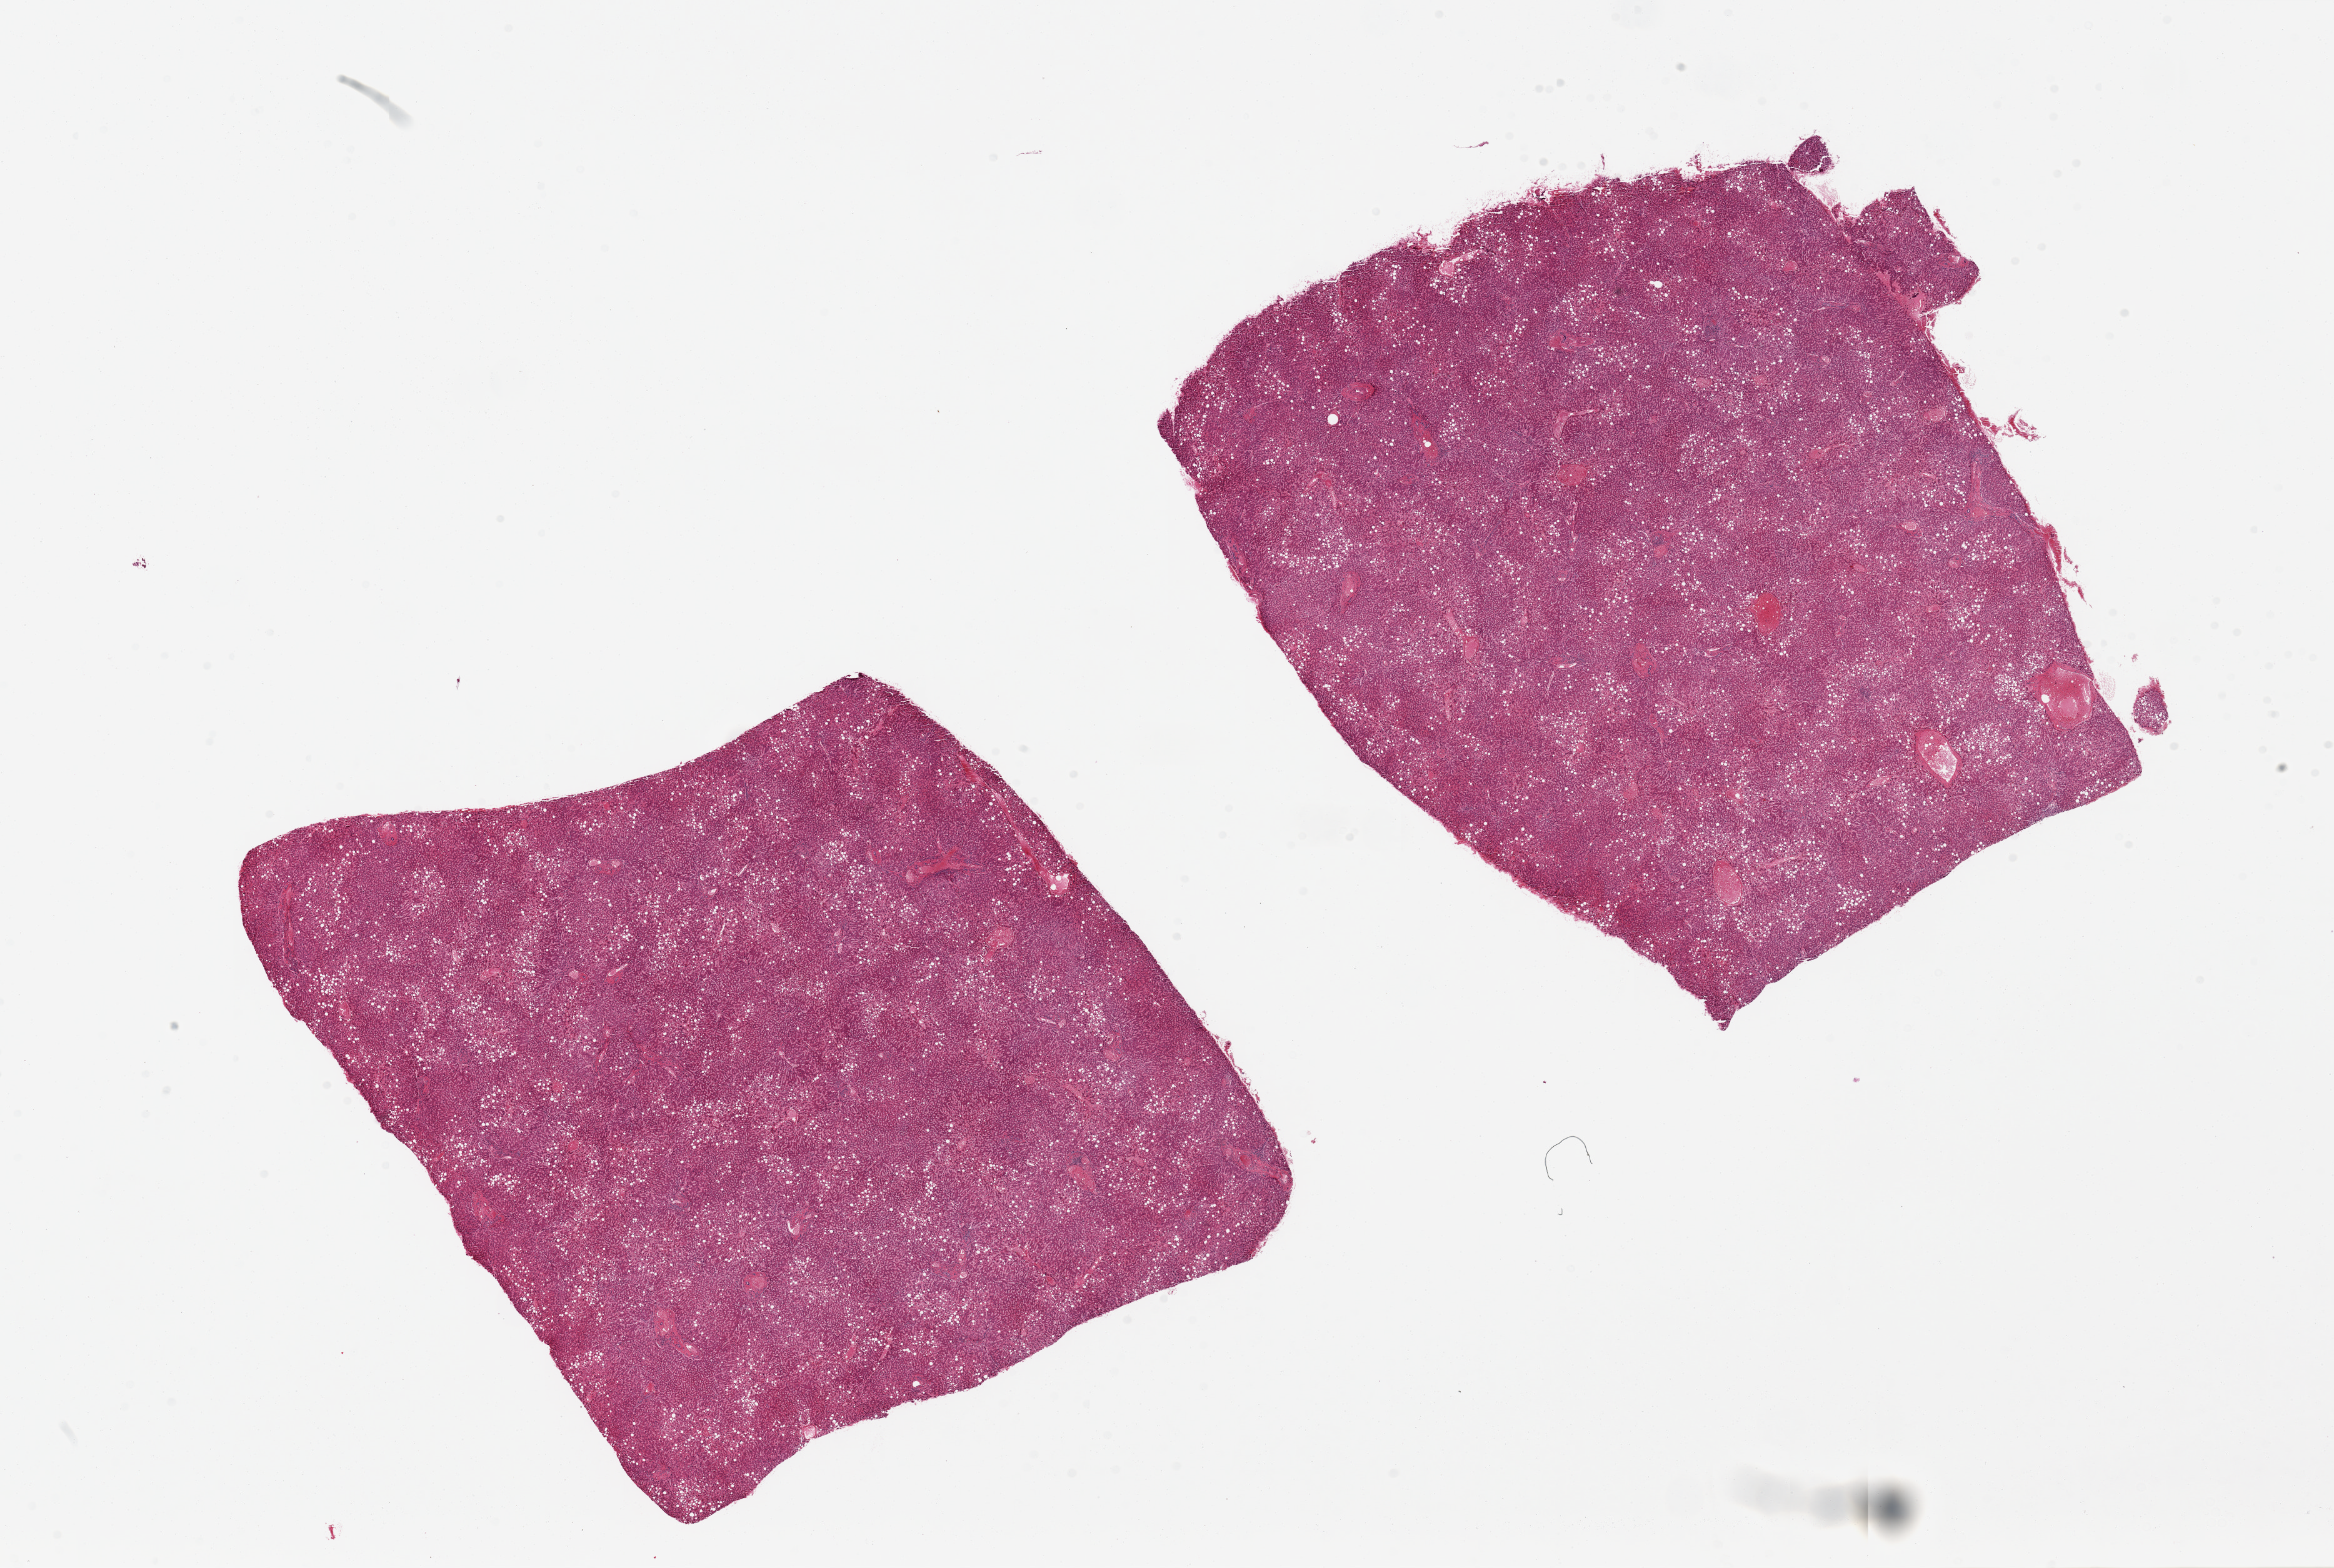
H&E whole-slide image, brightfield, whole scanned area (about 29.5 x 19.8 mm, slide scanned at 20x) shown as a low-resolution overview, PAXgene-fixed paraffin-embedded (PFPE) section, section of liver (target tissue), tissue donor sample.
- reviewer comment on this tissue sample: 2 pieces, 10x10 & 11x10mm; mild-moderate macrovesicular steatosis involving ~30-40% of parenchyma